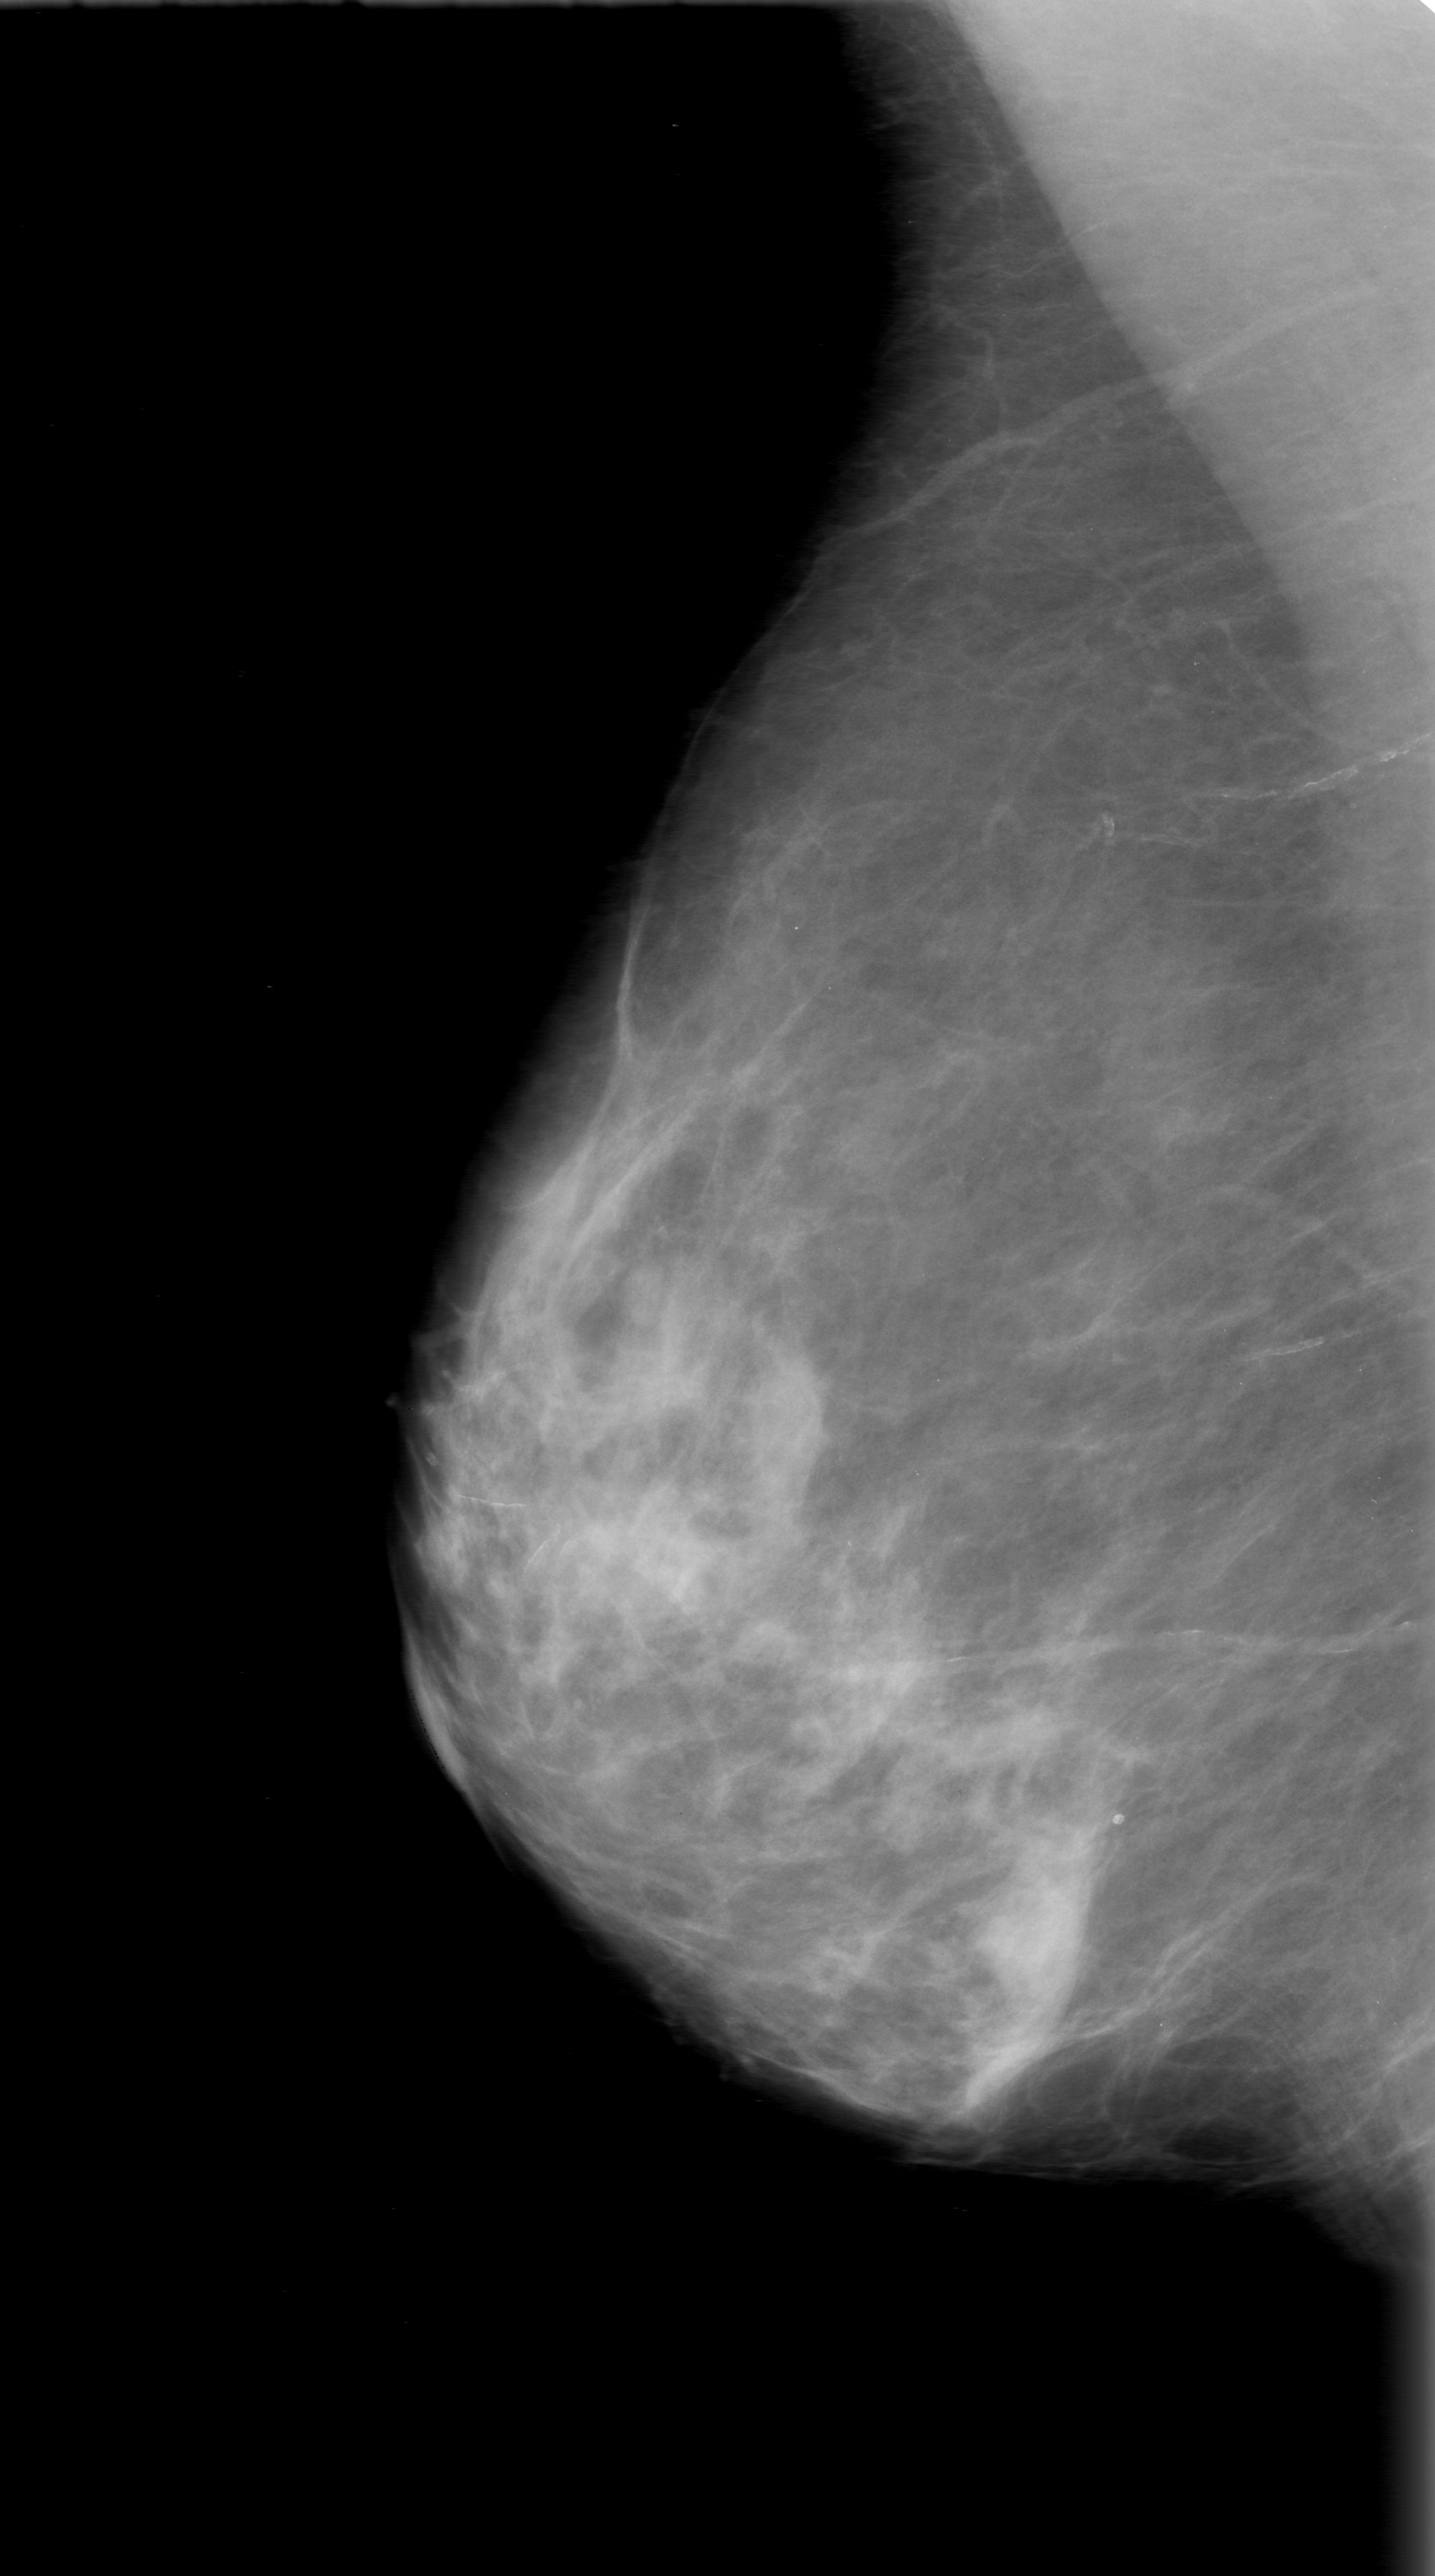
Scanned film-screen mammogram; right breast; MLO view; breast composition: scattered fibroglandular densities (BI-RADS density category 2 of 4).
- Mass, shape oval, margins obscured; BI-RADS assessment category 0 (incomplete: needs additional imaging); pathology (as recorded): benign.